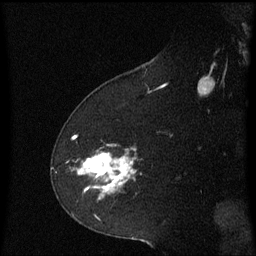
Breast MRI (dynamic contrast-enhanced), one sagittal slice. Slice 38 of 60 in the series (ordered by position). Dynamic contrast-enhanced series, image 2 of 3 at this slice position (ordered by acquisition). 1.5 T. TE 4.2 ms, TR 8.4 ms. 2.2 mm slice thickness. 256 × 256 image matrix, field of view 200 × 200 mm. Patient: female, 60 years. From the clinical record (not read from this slice): setting: breast cancer imaged before/during neoadjuvant chemotherapy; receptor status: triple-negative.
Structures marked on this image (semi-automatically segmented with operator editing):
- analysis volume of interest (the breast-tissue region the enhancement analysis was run in; not a lesion): bounding box (x1, y1, x2, y2) in pixels: (77, 144, 137, 201)
- tumour enhancement mask (voxels above the 70 % enhancement threshold inside the analysis volume of interest): (78, 152, 134, 191)